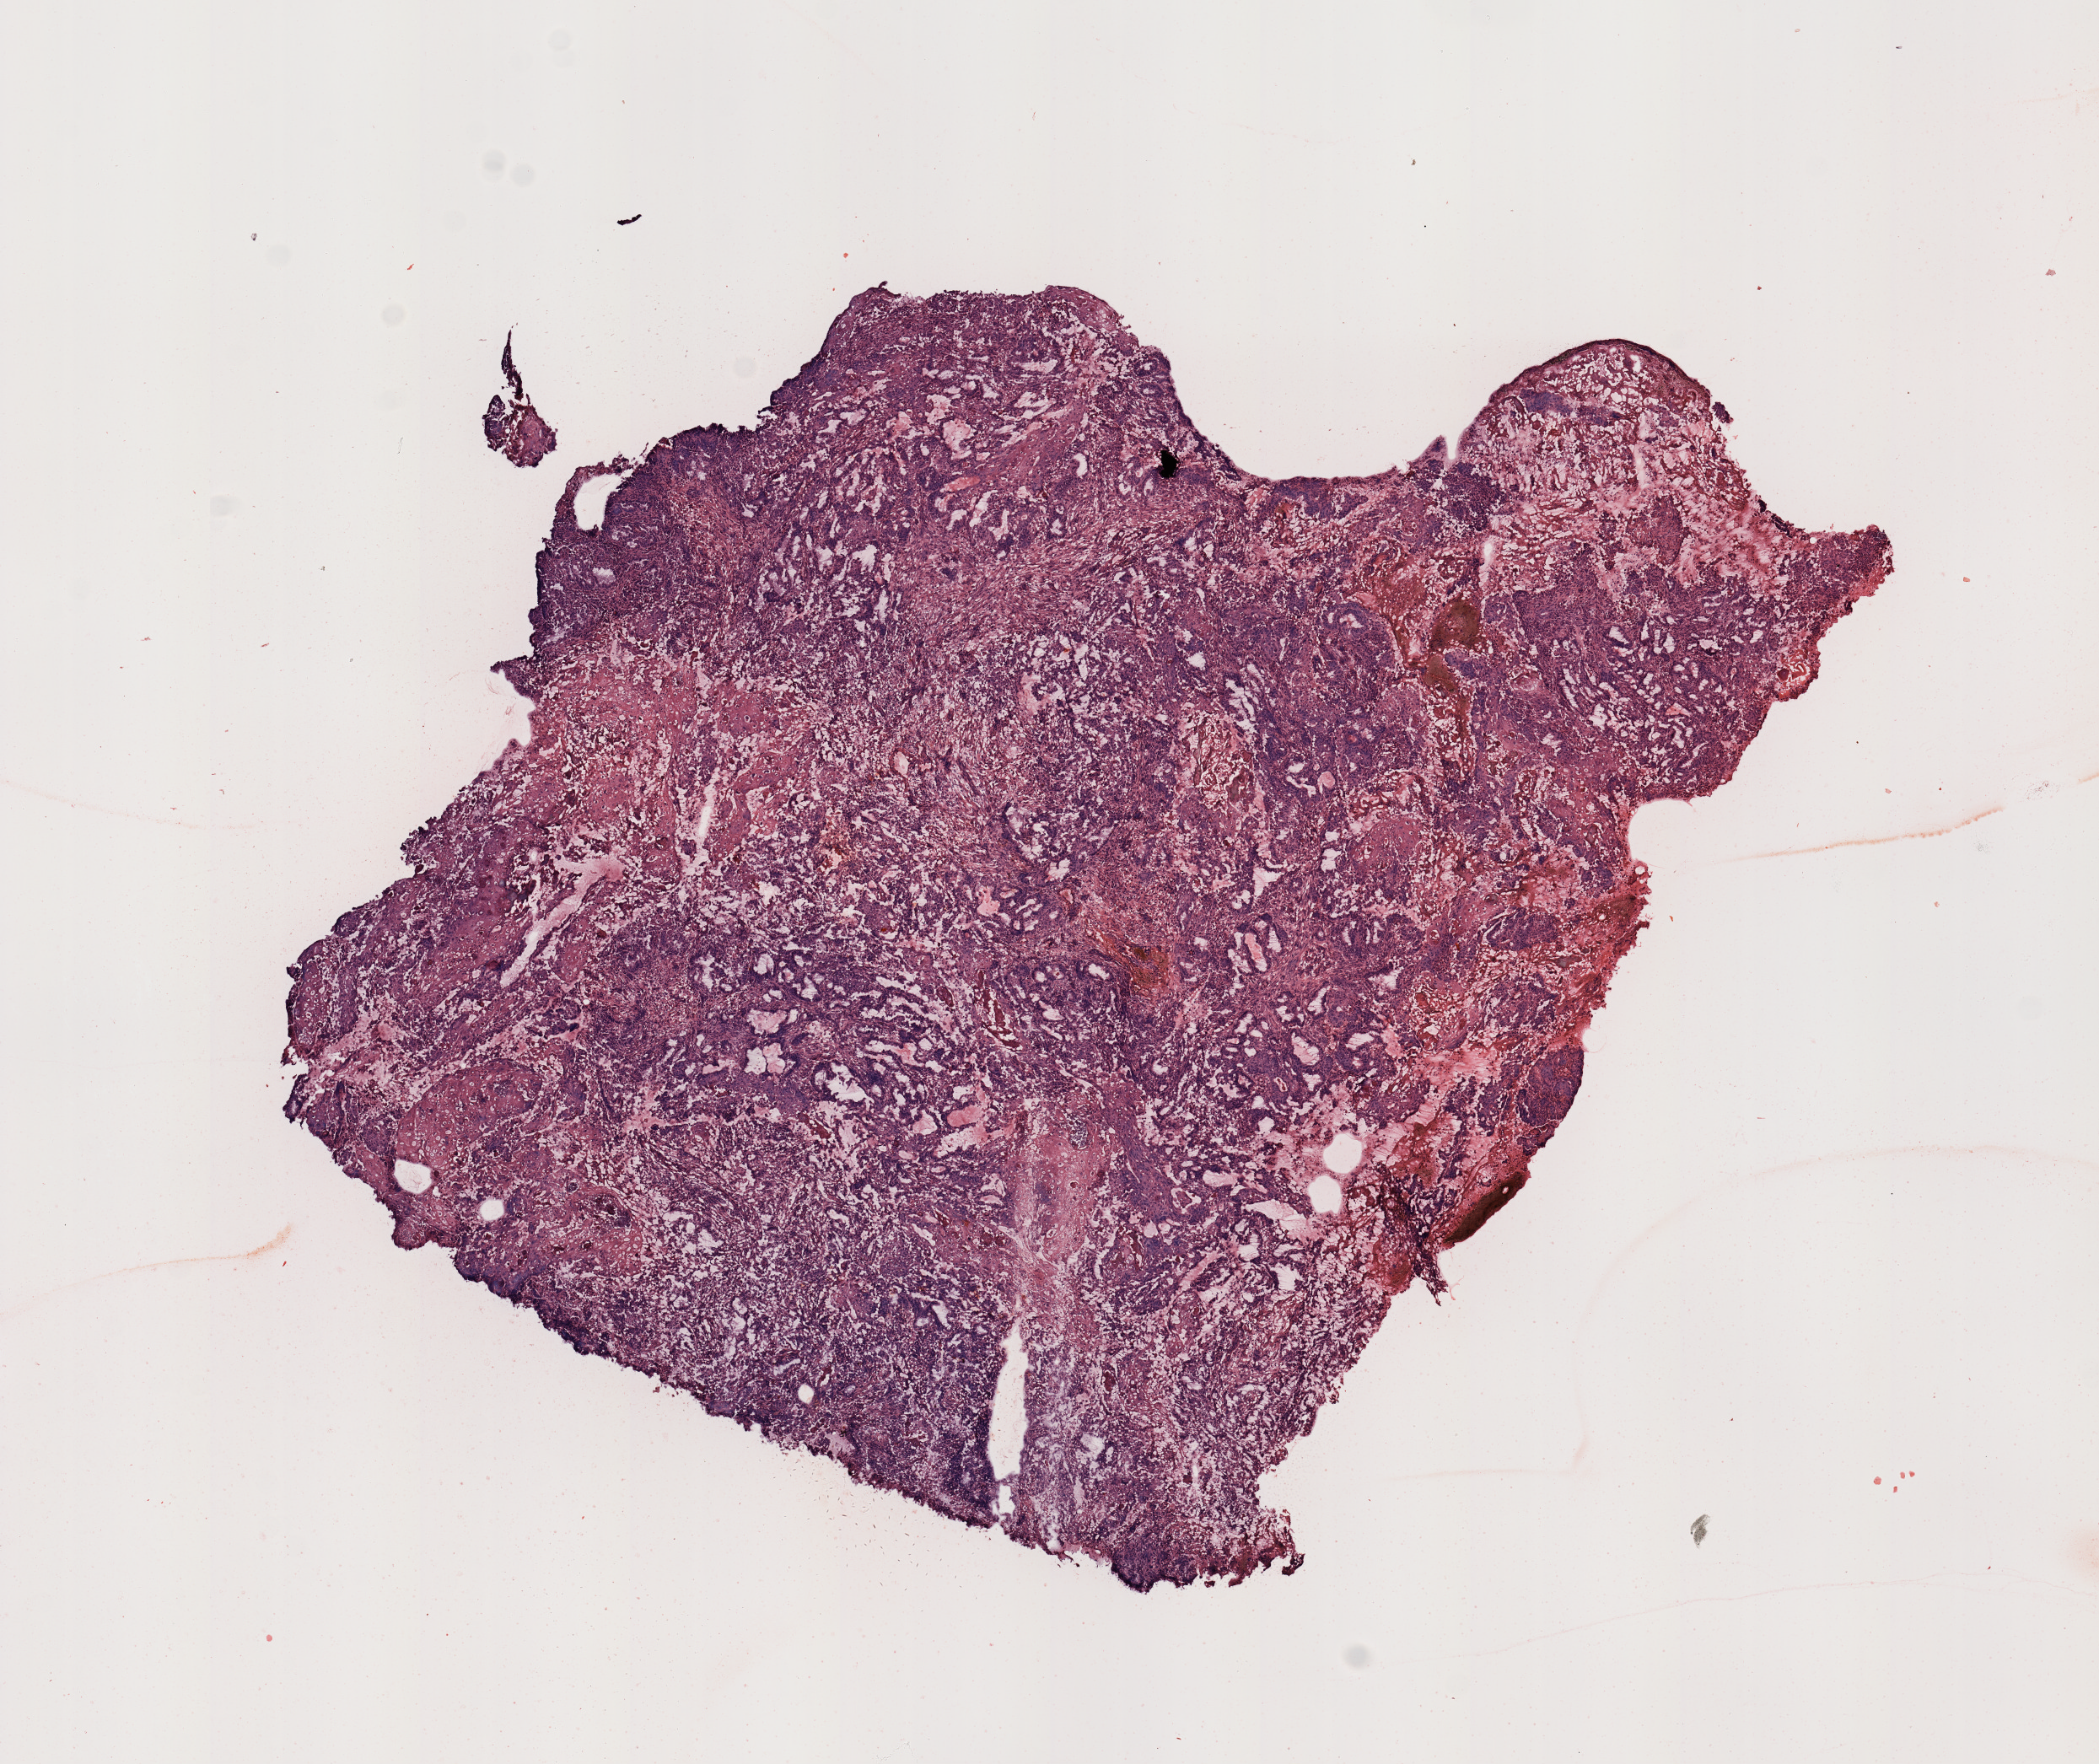
H&E whole-slide image, whole scanned area (about 9.8 x 8.3 mm, acquisition: 20x scan) shown as a low-resolution overview; uterus, tumour tissue. Female, 65 y/o.
Diagnosis: Endometrioid adenocarcinoma, NOS.